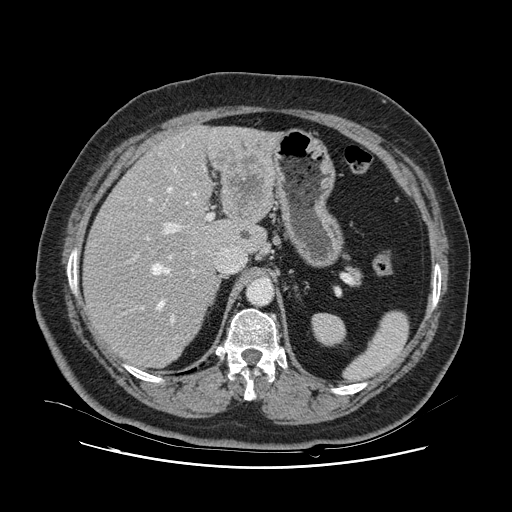
Contrast-enhanced abdominal CT, one axial slice; 120 kVp; intravenous contrast given; soft-tissue window (W 400 / L 40 HU); 2.5 mm slice thickness; 512 × 512 image matrix. Female patient, age 73 years. From the clinical record (not read from this slice): diagnosis: colorectal cancer liver metastases, imaged before liver resection; multiple liver metastases: no; largest metastasis: 7 cm; chemotherapy before resection: yes.
Structures marked on this image (expert manual segmentation):
- hepatic veins: bounding box (x1, y1, x2, y2) in pixels: (152, 145, 196, 309)
- liver: (84, 127, 273, 368)
- planned liver remnant (the part of the liver to remain after resection): (84, 157, 241, 368)
- portal vein (with intrahepatic branches): (132, 198, 213, 323)
- liver metastasis: (241, 232, 251, 241)
- liver metastasis: (215, 141, 264, 214)